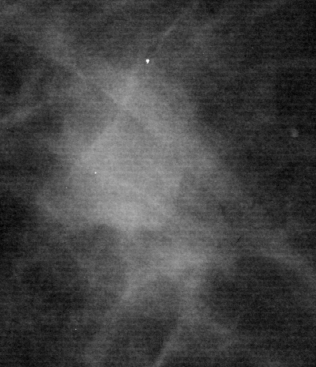
Cropped region of a digitized screen-film mammogram centred on a radiologist-marked abnormality, right breast, CC view.
Finding: mass, shape lobulated, margins microlobulated; BI-RADS assessment category 5; subtlety rating 5 on a 1 (subtle) to 5 (obvious) scale; pathology result (as recorded, not read from the image): malignant.